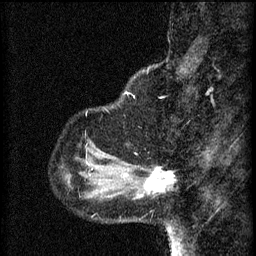
Breast MRI (dynamic contrast-enhanced), one sagittal slice. Slice 12 of 60 in the series (ordered by position). 3 images stored at this slice position (order not interpretable as contrast timing). 1.5 T. TE 4.2 ms, TR 8.2 ms. 256 × 256 image matrix, field of view 180 × 180 mm. Patient: female, 37 years.
Structures marked on this image (semi-automatic segmentation, software-assisted and operator-edited):
- analysis volume of interest (the breast-tissue region the enhancement analysis was run in; not a lesion): bounding box [x1, y1, x2, y2] px = [126, 164, 175, 201]
- tumour enhancement mask (voxels above the 70 % enhancement threshold inside the analysis volume of interest): [126, 168, 174, 199]